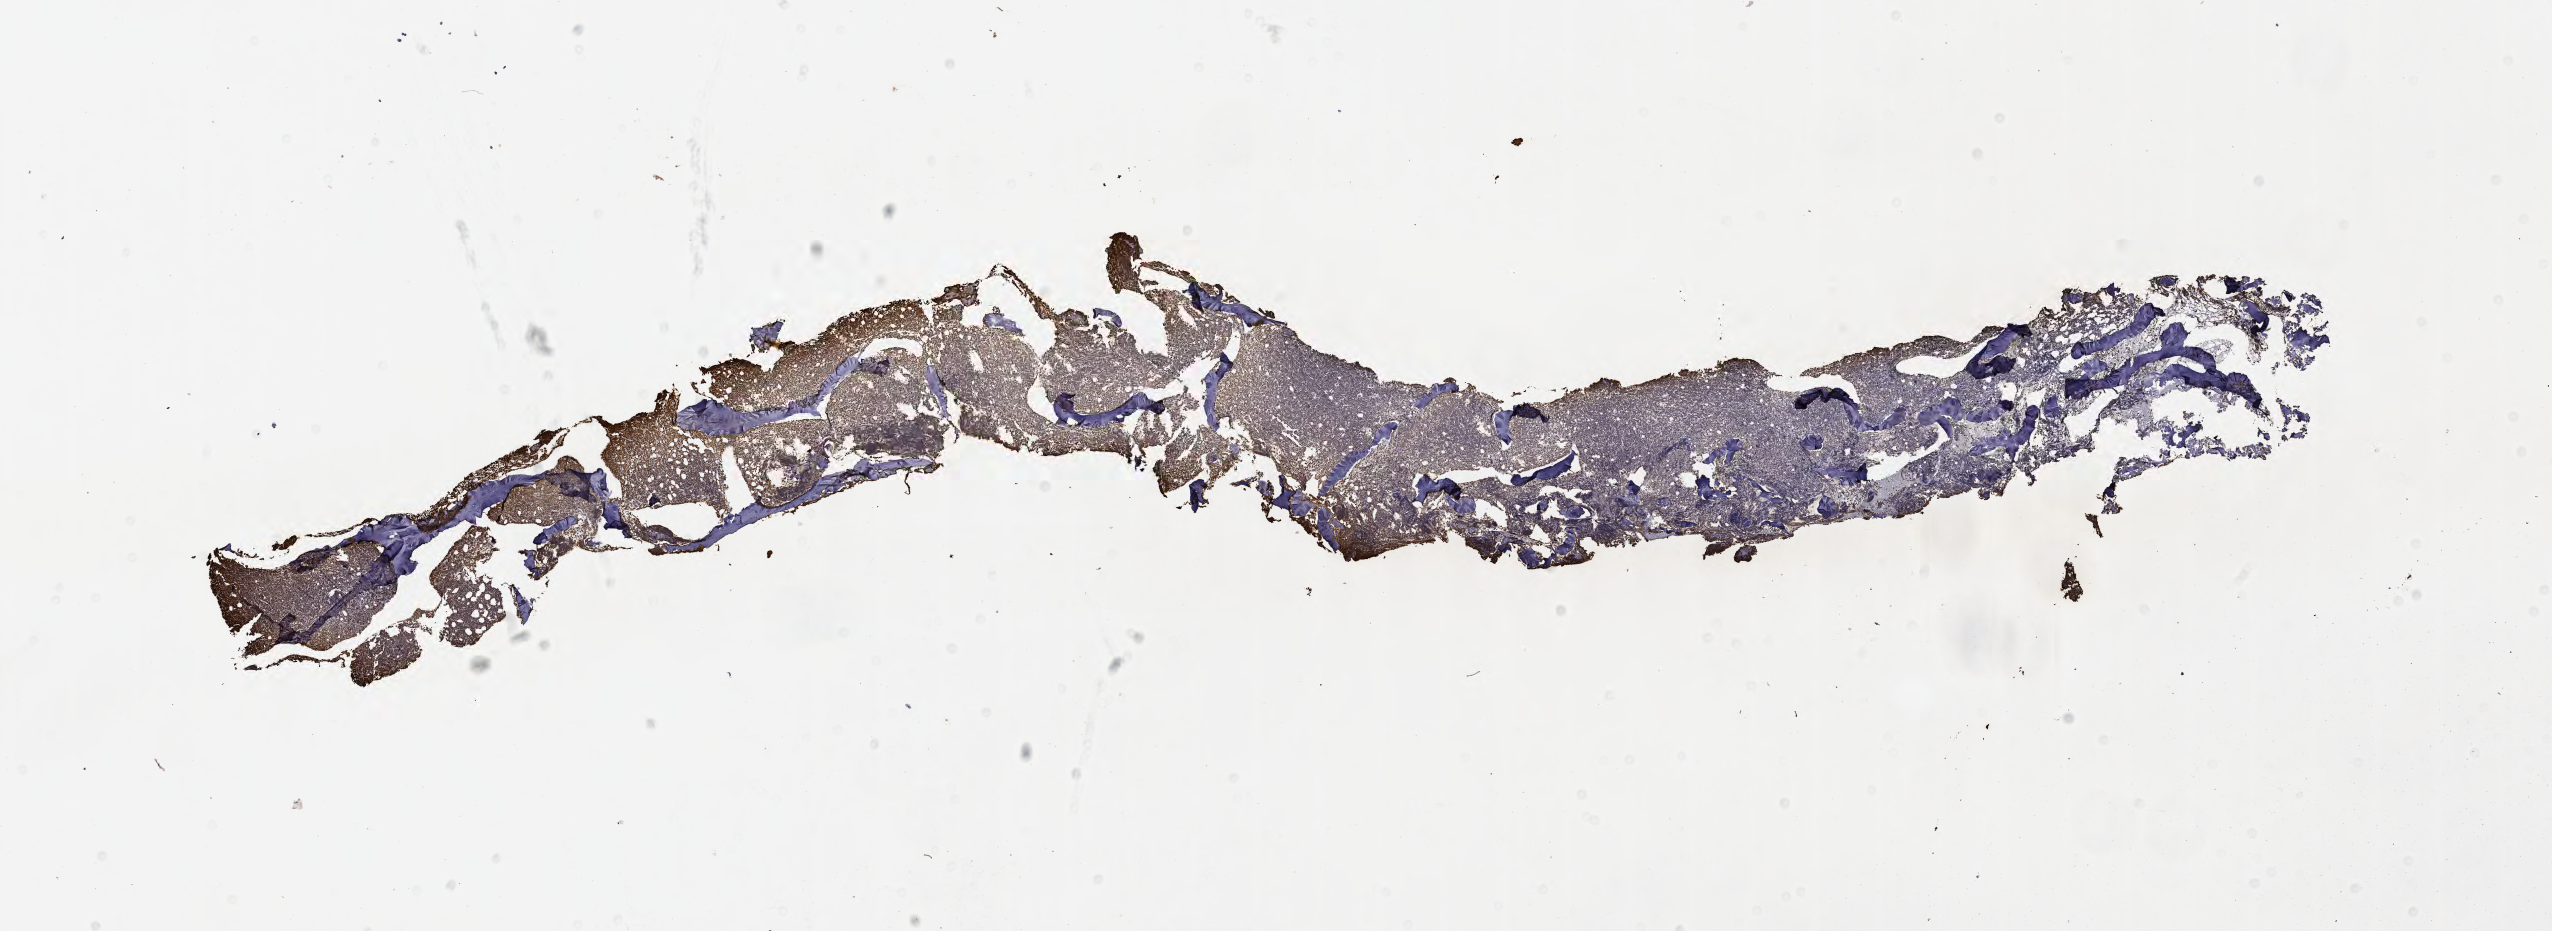
Immunohistochemistry (IHC) whole-slide image stained for Ki-67 — whole scanned area (about 20.6 x 7.5 mm) shown as a low-resolution overview. Tumor tissue. Male patient.
Diagnosis: Burkitt lymphoma, NOS.